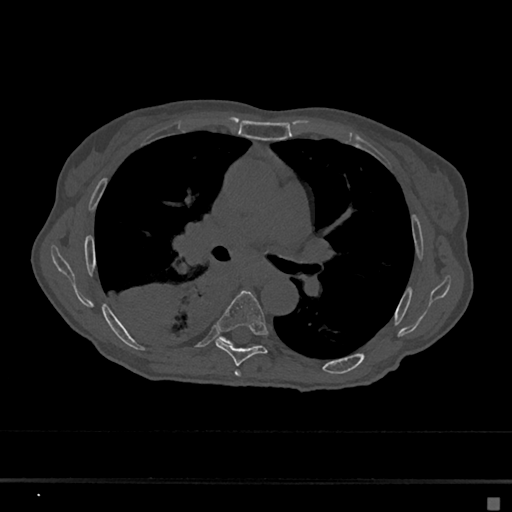
CT including the spine, one axial slice. Position 411 of 797 along the scan axis. Bone window (W 1800 / L 400 HU). 0.5 mm slice thickness. 512 × 512 image matrix. Patient: female, 68 years. Case-level facts recorded for this patient, not image findings: primary cancer: renal.
Outlined on this slice (semi-automatically segmented with operator editing):
- T5 vertebra: bounding box [x1, y1, x2, y2] px = [234, 370, 241, 377]
- T6 vertebra: [215, 291, 268, 366]
- T7 vertebra: [221, 337, 232, 344]